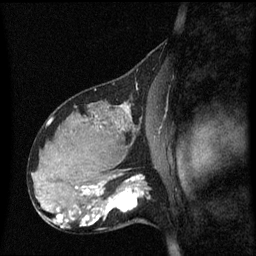
Breast MRI (dynamic contrast-enhanced), one sagittal slice. Position 35 of 60 along the scan axis. Dynamic contrast-enhanced series, image 2 of 3 at this slice position (ordered by acquisition). 1.5 T. TE 4.2 ms, TR 8.4 ms. 2.1 mm slice thickness. 256 × 256 image matrix, field of view 210 × 210 mm. Patient: female, 31 years. Case-level facts recorded for this patient, not image findings: setting: breast cancer imaged before/during neoadjuvant chemotherapy; receptor status: HR-positive, HER2-negative.
Outlined on this slice (semi-automatically segmented with operator editing):
- analysis volume of interest (the breast-tissue region the enhancement analysis was run in; not a lesion): bounding box (x1, y1, x2, y2) in pixels: (98, 175, 152, 228)
- tumour enhancement mask (voxels above the 70 % enhancement threshold inside the analysis volume of interest): (98, 177, 145, 220)